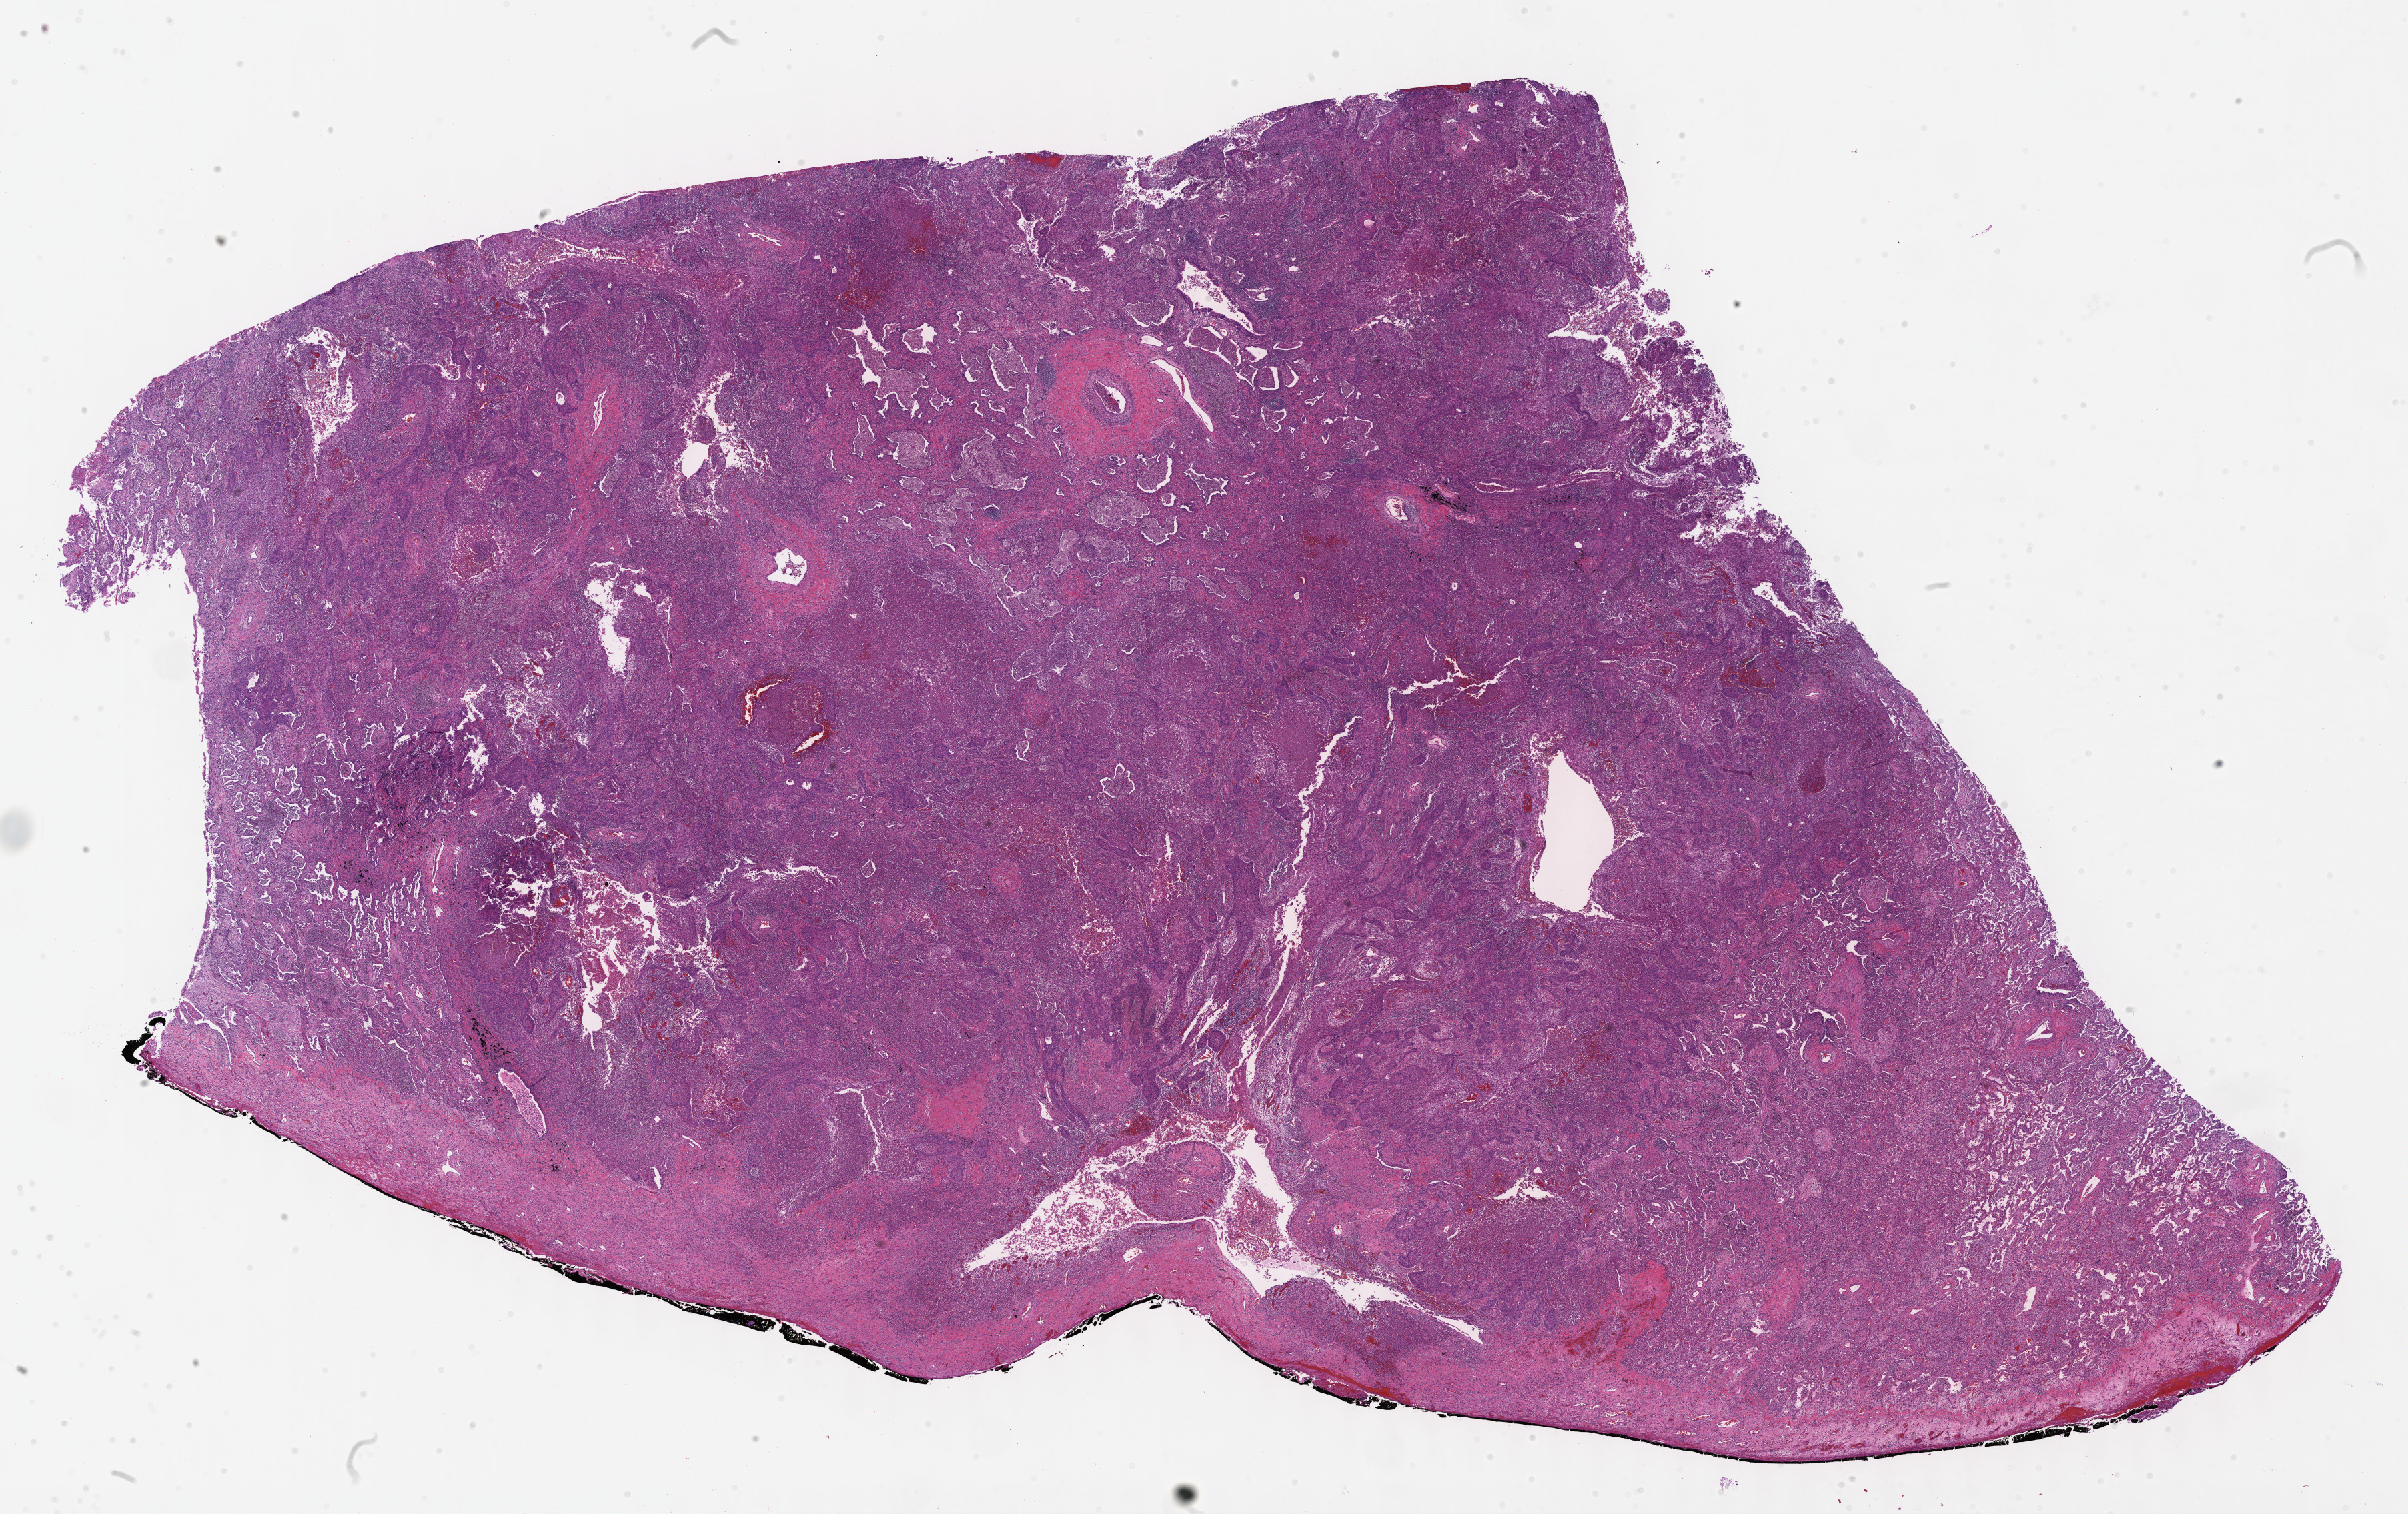
Whole-slide histology image, H&E — low-resolution overview of the scanned area, about 29.2 x 18.3 mm (slide scanned at 40x); formalin-fixed paraffin-embedded (FFPE) diagnostic section; primary tumour sample from the lung. Patient: female, age at initial diagnosis 57 years.
Diagnosis: Squamous cell carcinoma, NOS. Laterality: right. AJCC pathologic stage: IA (5th edition).